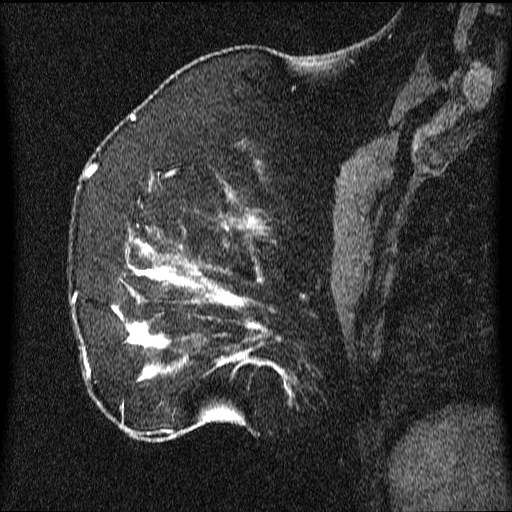
Breast MRI (dynamic contrast-enhanced), one sagittal slice; slice 18 of 64 in the series (ordered by position); dynamic contrast-enhanced series, image 2 of 3 at this slice position (ordered by acquisition); 1.5 T; TE 4.2 ms, TR 9.1 ms; 2.2 mm slice thickness; 512 × 512 image matrix, field of view 180 × 180 mm. Patient: female, 52 years.
Structures marked on this image (semi-automatically segmented with operator editing):
- analysis volume of interest (the breast-tissue region the enhancement analysis was run in; not a lesion): bounding box [x1, y1, x2, y2] px = [71, 203, 349, 438]
- tumour enhancement mask (voxels above the 70 % enhancement threshold inside the analysis volume of interest): [84, 218, 288, 432]